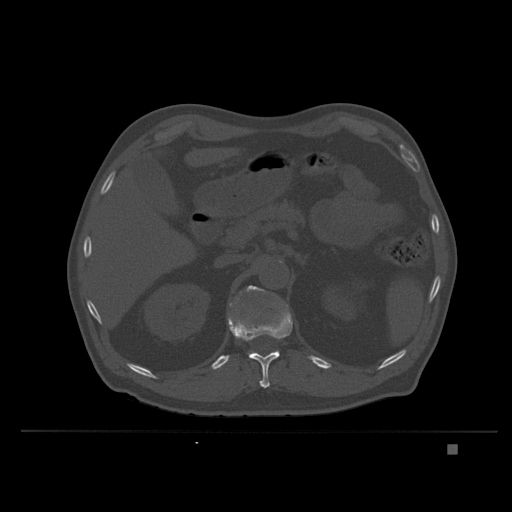
CT including the spine, one axial slice. Position 154 of 435 along the scan axis. Bone window (W 1800 / L 400 HU). 512 × 512 image matrix. Patient: male, 73 years. Case-level facts recorded for this patient, not image findings: primary cancer: skin.
Structures marked on this image (semi-automatically segmented with operator editing):
- L1 vertebra: bounding box (x1, y1, x2, y2) in pixels: (229, 291, 279, 355)
- T12 vertebra: (228, 309, 293, 388)